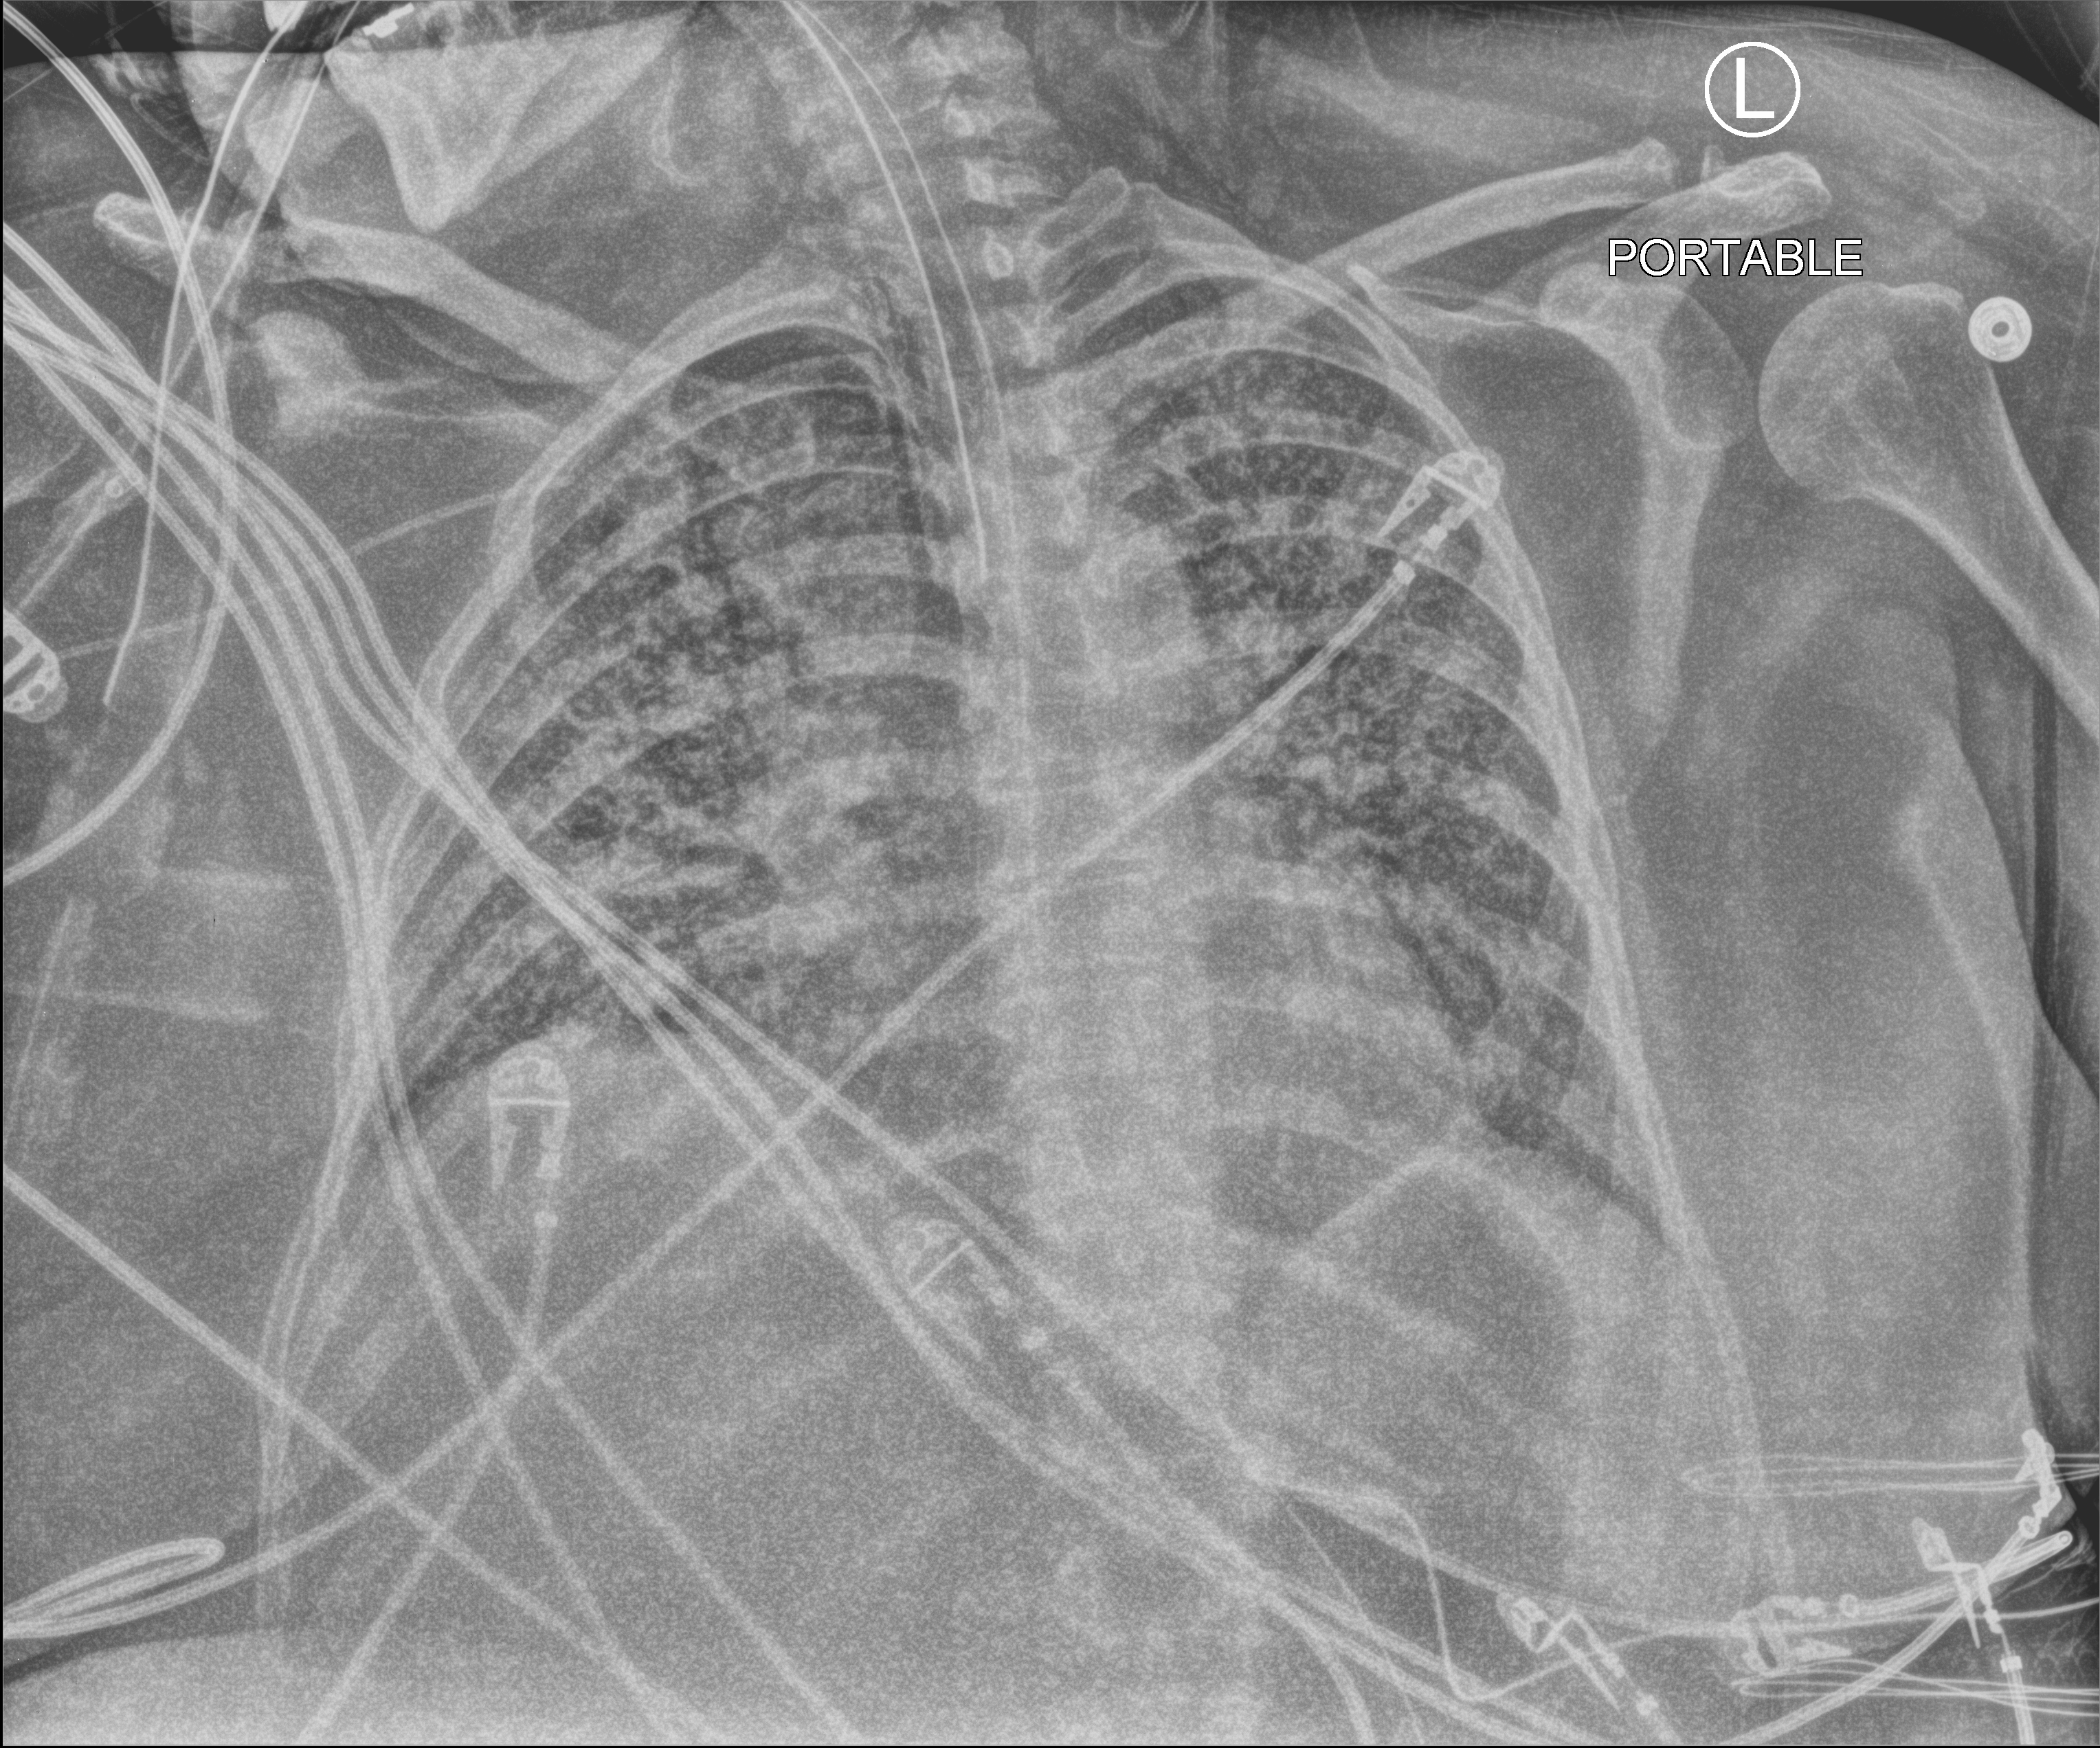
Chest X-ray (portable). Female patient hospitalised with COVID-19, age 18–59 years.
From the hospital-stay record, not from the radiograph (when in the stay this image was taken is not recorded):
- length of hospital stay: 95 days
- mechanically ventilated during this hospital stay: yes
- admitted to intensive care during this hospital stay: yes